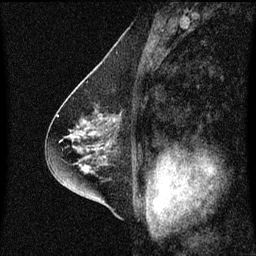
Breast MRI (dynamic contrast-enhanced), one sagittal slice; position 37 of 60 along the scan axis; dynamic contrast-enhanced series, image 2 of 3 at this slice position (ordered by acquisition); 1.5 T; TE 4.2 ms, TR 8.4 ms; 2 mm slice thickness; 256 × 256 image matrix. Female patient, age 58 years.
Outlined on this slice (semi-automatically segmented with operator editing):
- analysis volume of interest (the breast-tissue region the enhancement analysis was run in; not a lesion): bounding box [x1, y1, x2, y2] px = [86, 94, 122, 143]
- tumour enhancement mask (voxels above the 70 % enhancement threshold inside the analysis volume of interest): [113, 120, 116, 123]